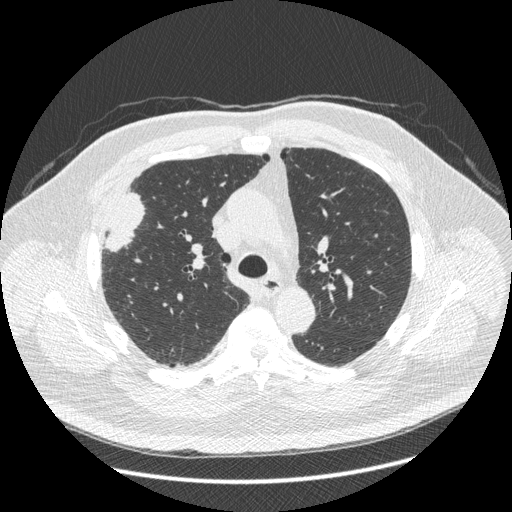
Low-dose screening chest CT, one axial slice. Slice 292 of 426 in the series (ordered by position). Reconstruction kernel STANDARD. 120 kVp. Lung window (W 1500 / L -600 HU). 512 × 512 image matrix.
Outlined on this slice (manually delineated by an expert):
- lesion 1 (tumor, upper lobe of right lung): bounding box (x1, y1, x2, y2) in pixels: (105, 192, 145, 252)